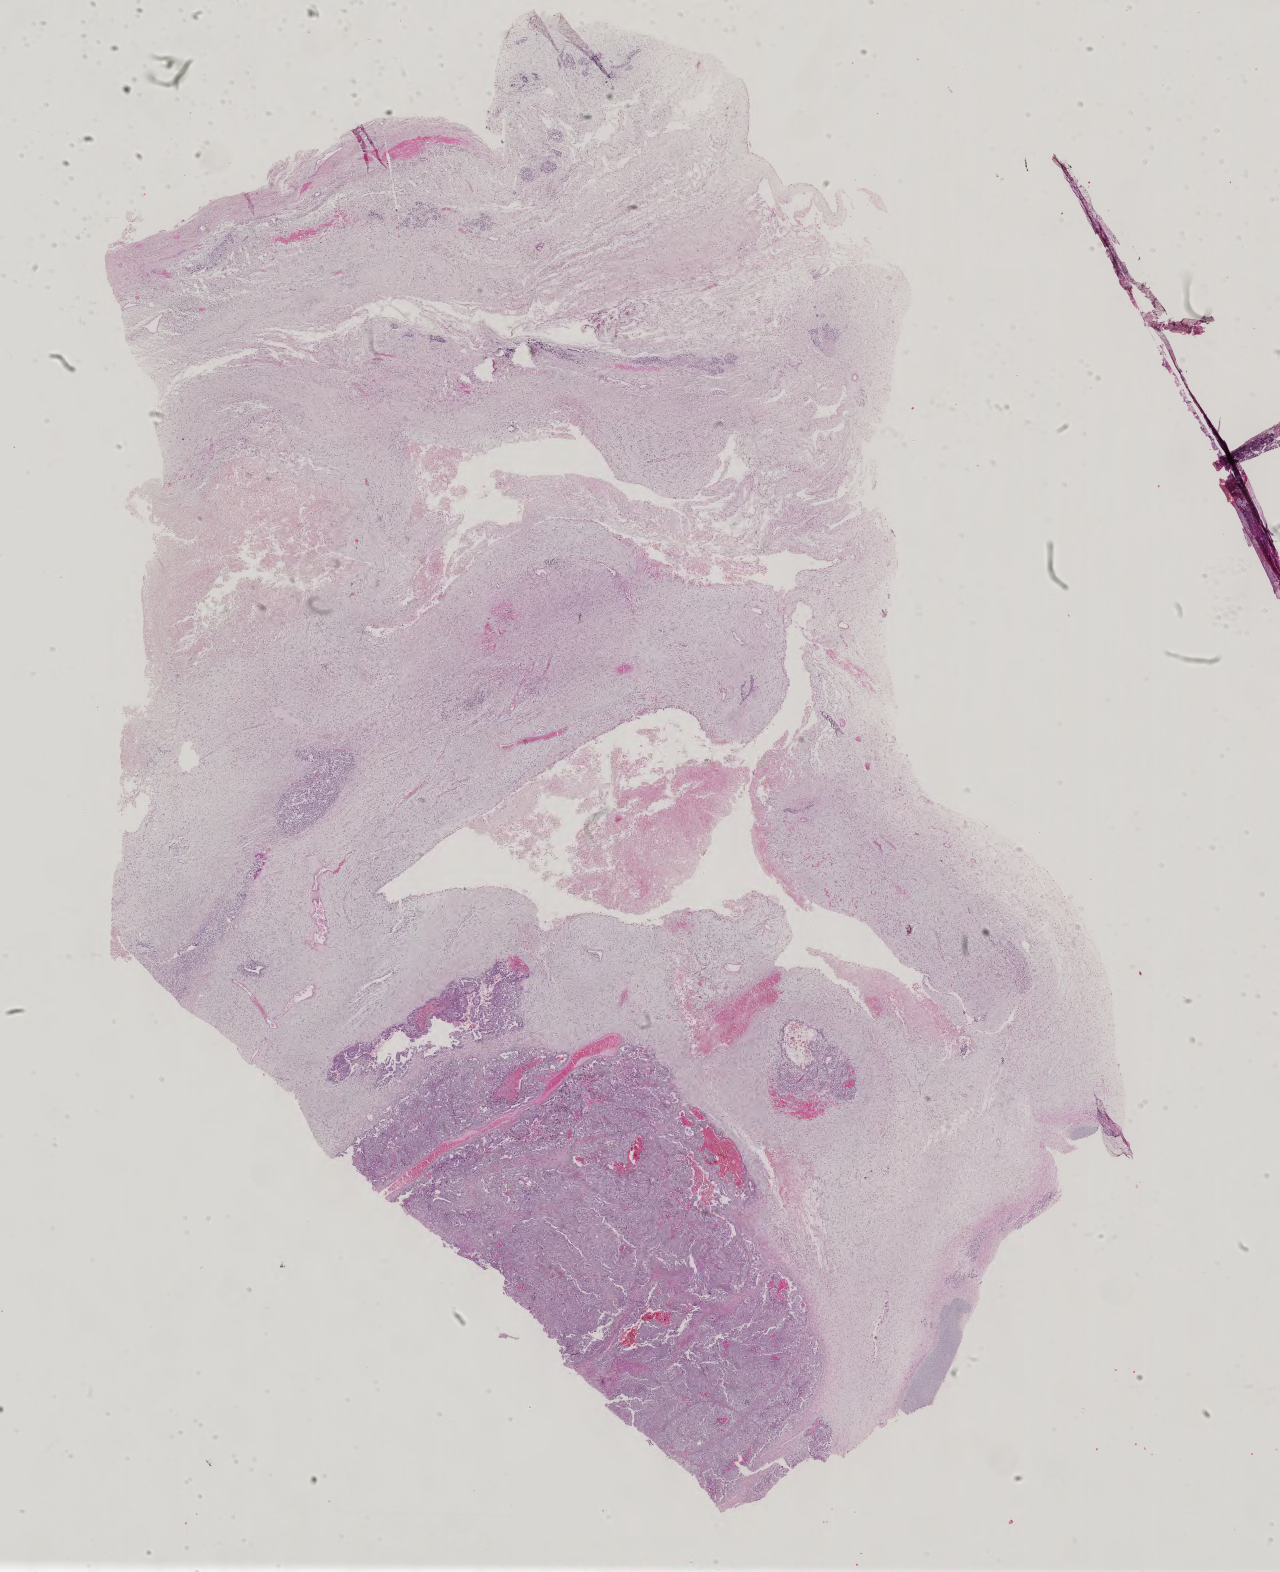
H&E-stained whole-slide image, shown as a low-resolution overview of the whole scanned area (about 18.7 x 22.9 mm, acquisition: 40x scan). Formalin-fixed paraffin-embedded (FFPE) diagnostic section. Sample: primary tumour, testis. Patient: male, age at initial diagnosis 21 years.
- pathologic diagnosis: Embryonal carcinoma, NOS
- AJCC pathologic stage: IS (6th edition)